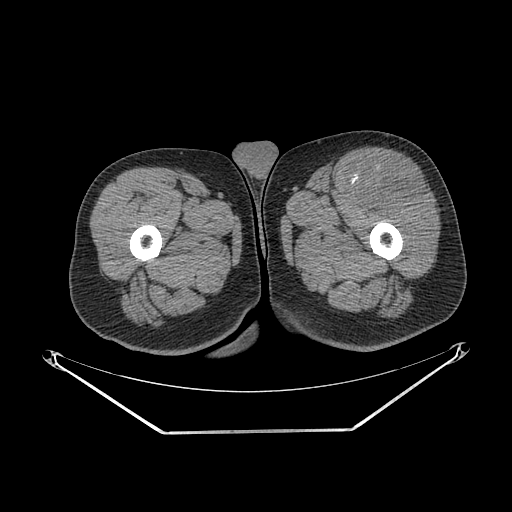
CT of an extremity soft-tissue mass (from a PET/CT study), one axial slice; slice 248 of 267 in the series (ordered by position); 140 kVp; soft-tissue window (W 400 / L 40 HU); 512 × 512 image matrix, field of view 500 × 500 mm. Male patient. Case-level facts recorded for this patient, not image findings: histological type: extraskeletal osteosarcoma; grade: high; site of the primary tumour: thigh.
Structures marked on this image (expert contour drawn on MRI and transferred to this co-registered scan by the dataset authors):
- gross tumour volume (mass): box from (x=356, y=165) to (x=426, y=207) px